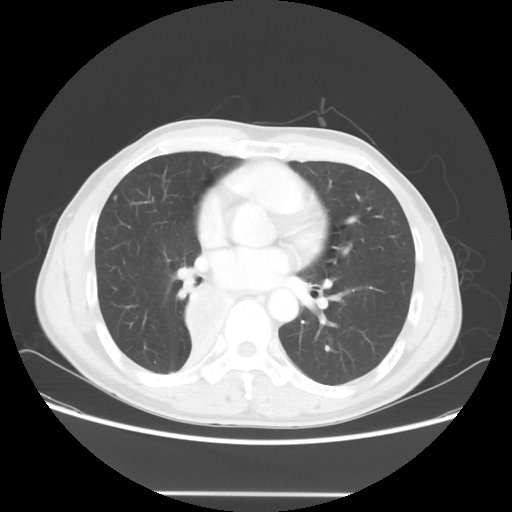
Chest CT, one axial slice. Slice 30 of 62 in the series (ordered by position). Reconstruction kernel STANDARD. Lung window (W 1500 / L -600 HU). 5 mm slice thickness. 512 × 512 image matrix, field of view 393 × 393 mm. Male patient, age 47 years. From the clinical record (not read from this slice): clinical TNM (as recorded): T2 N0 M0.
Structures marked on this image (rectangle marked by the reading radiologist):
- lung tumour (recorded histology: squamous cell carcinoma): bounding box <176,283,246,345> (left, top, right, bottom; pixels)